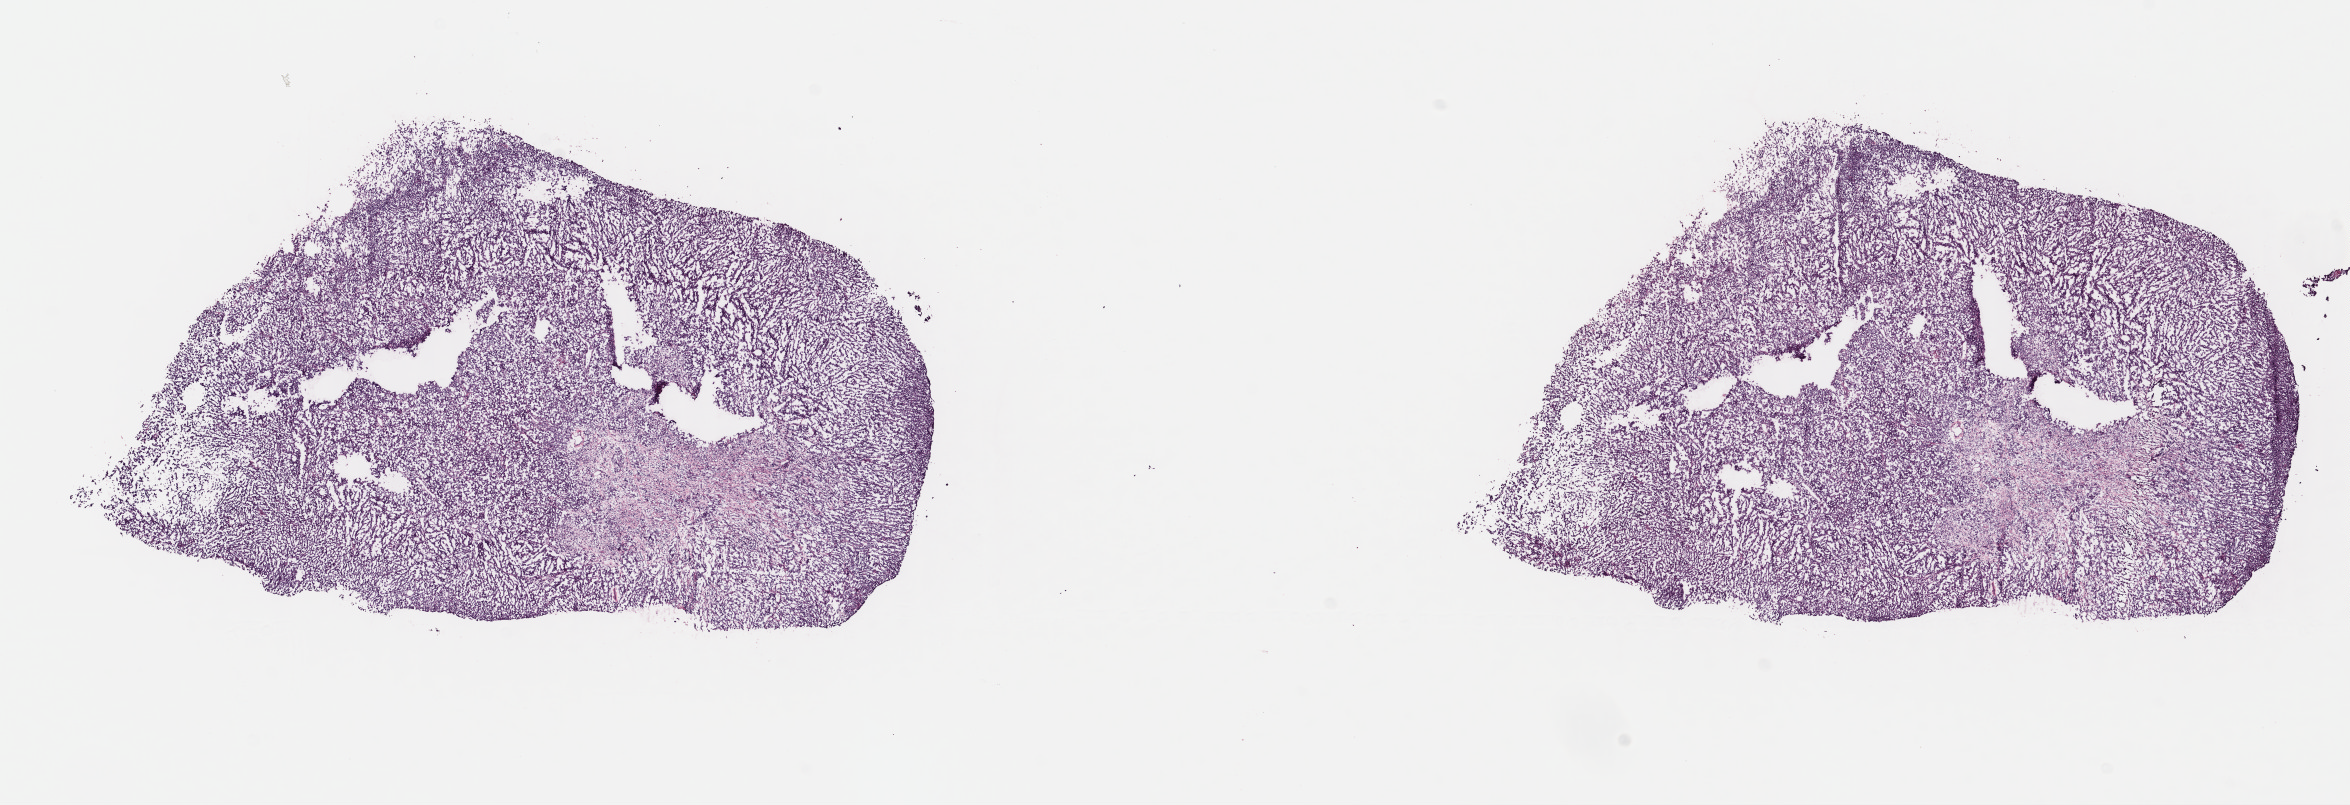
Whole-slide histology image, H&E — whole scanned area (about 18.5 x 6.3 mm) shown as a low-resolution overview, frozen section from the top of the tissue portion, metastatic tumour sample, sampled site not recorded. Female, age 39 years at initial diagnosis.
This section: metastatic tumour tissue. Patient diagnosis: Malignant melanoma, NOS.